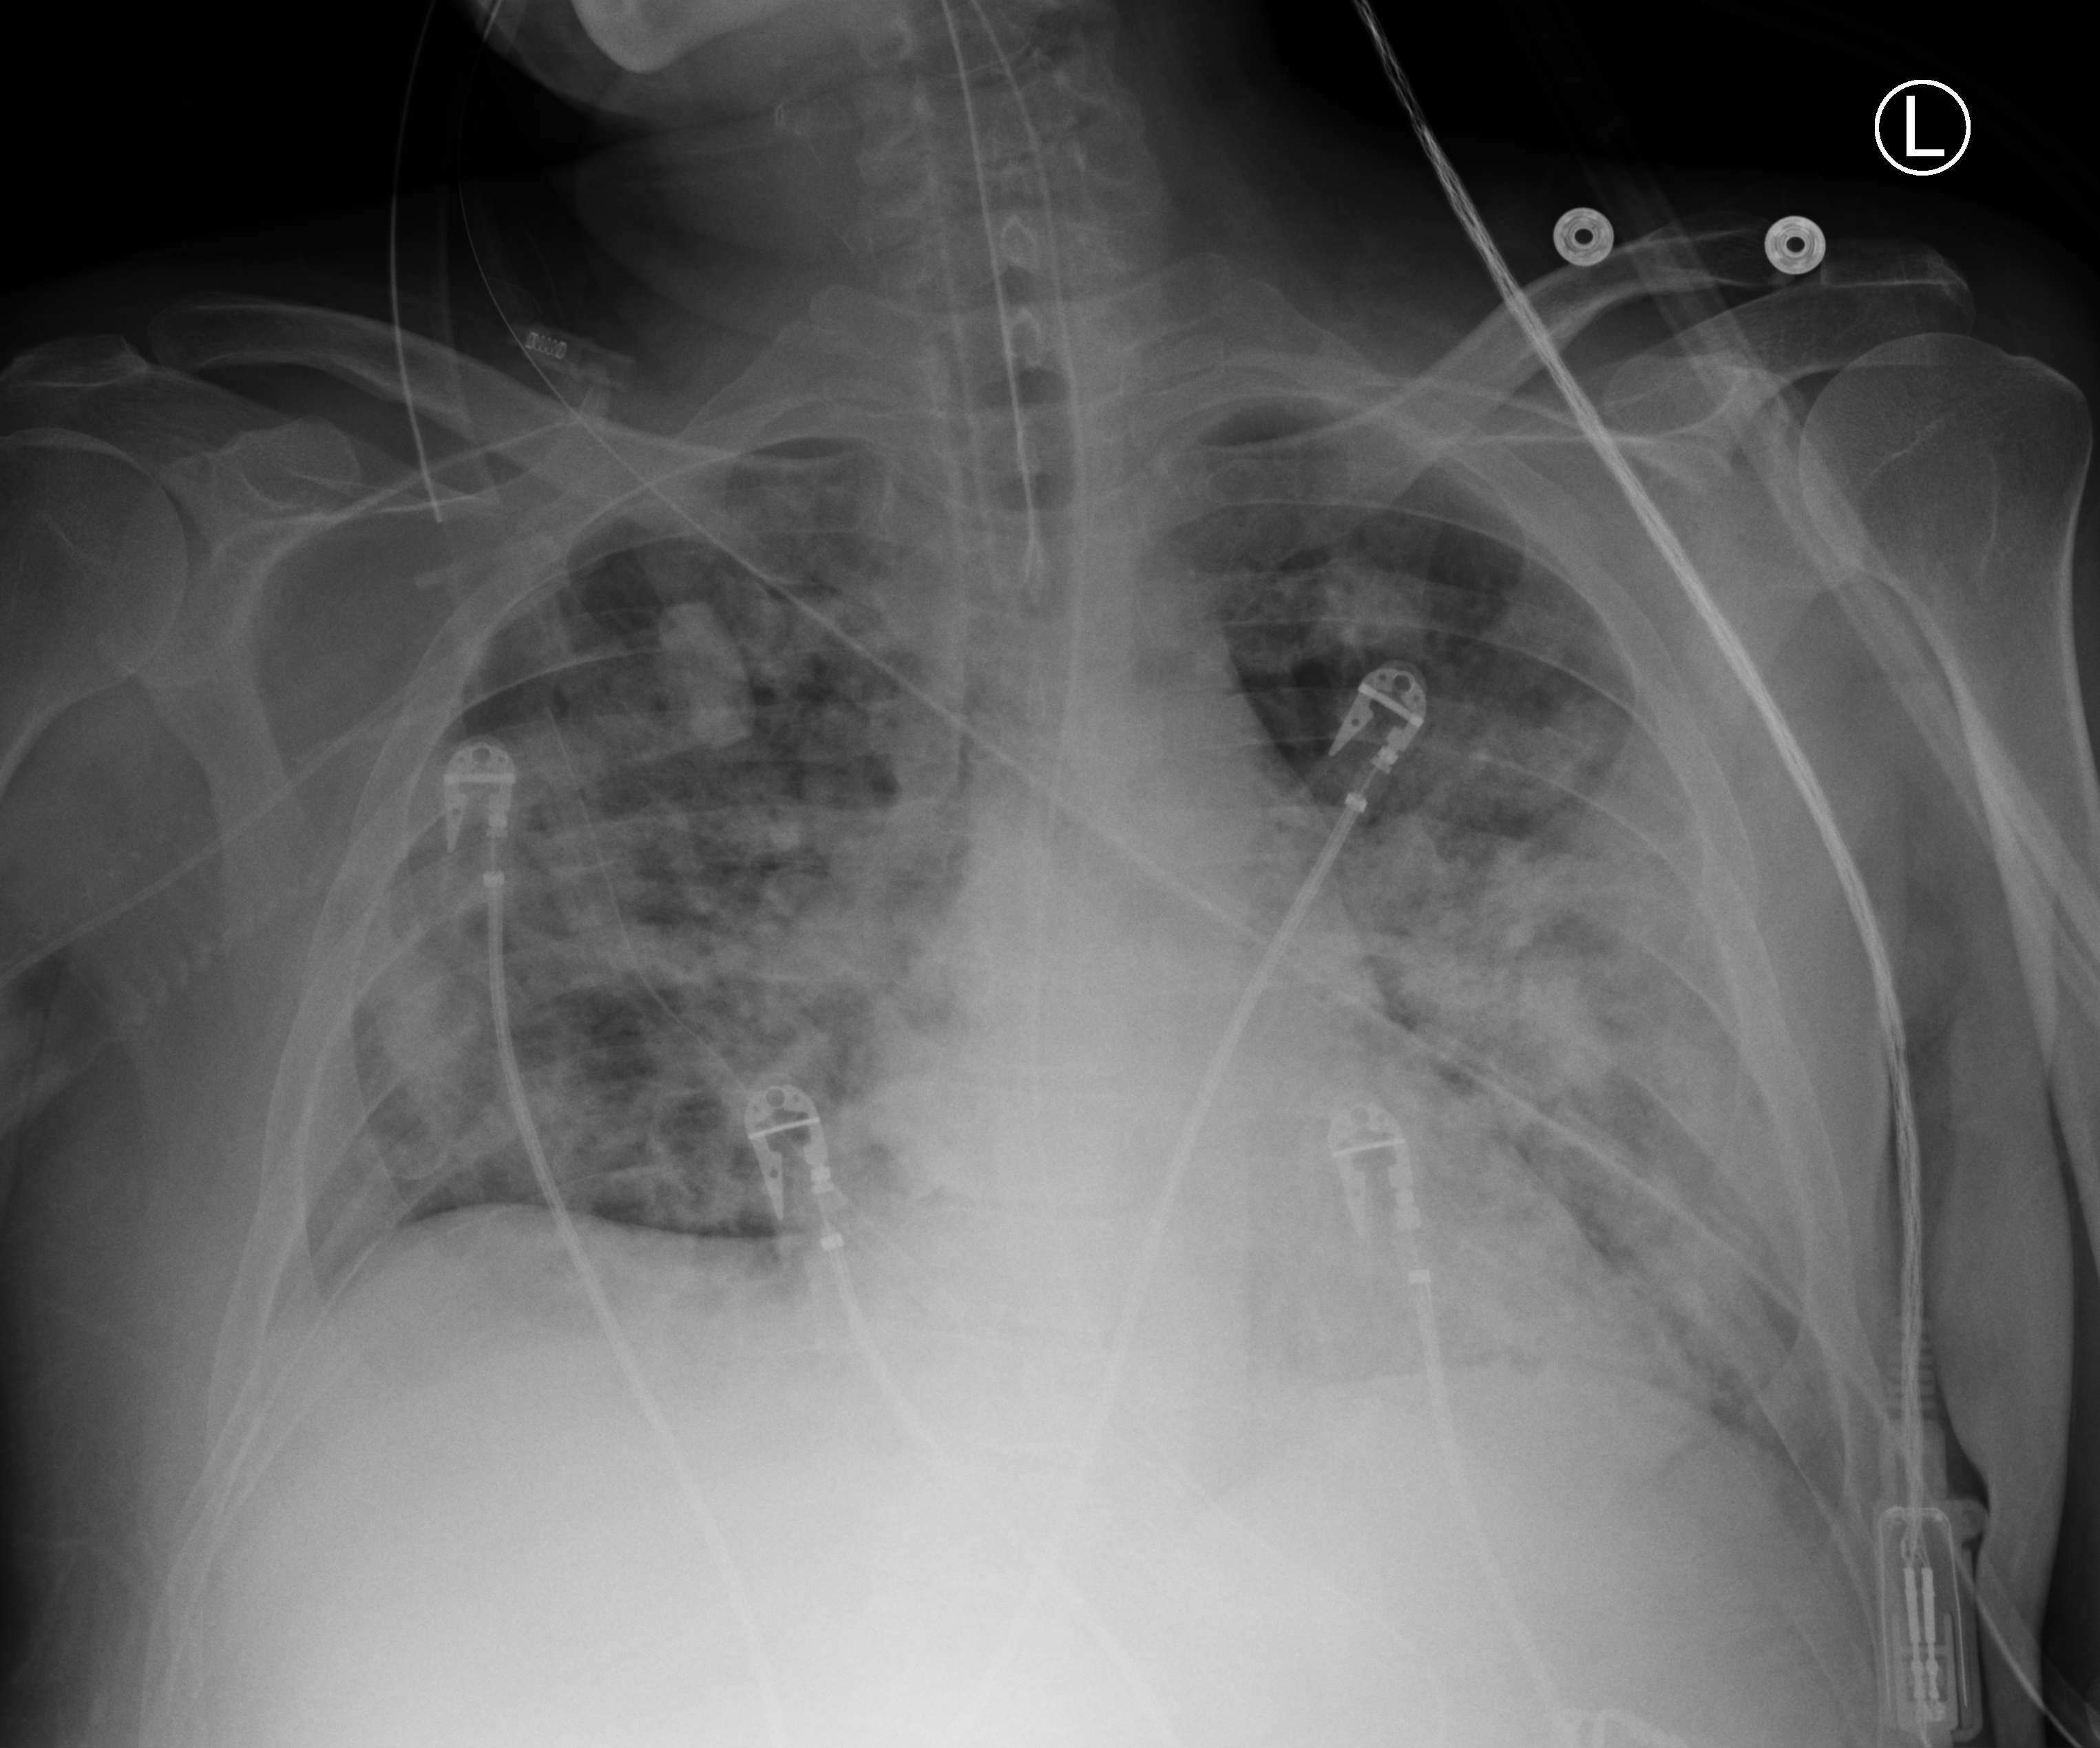
Chest X-ray (portable); anteroposterior (AP) projection. Patient hospitalised with COVID-19; male, aged 18–59 years.
Admission-level facts for this patient (not findings on this image; timing relative to this image not recorded): length of hospital stay: 20 days; COPD (admission record): no; mechanically ventilated during this hospital stay: yes.